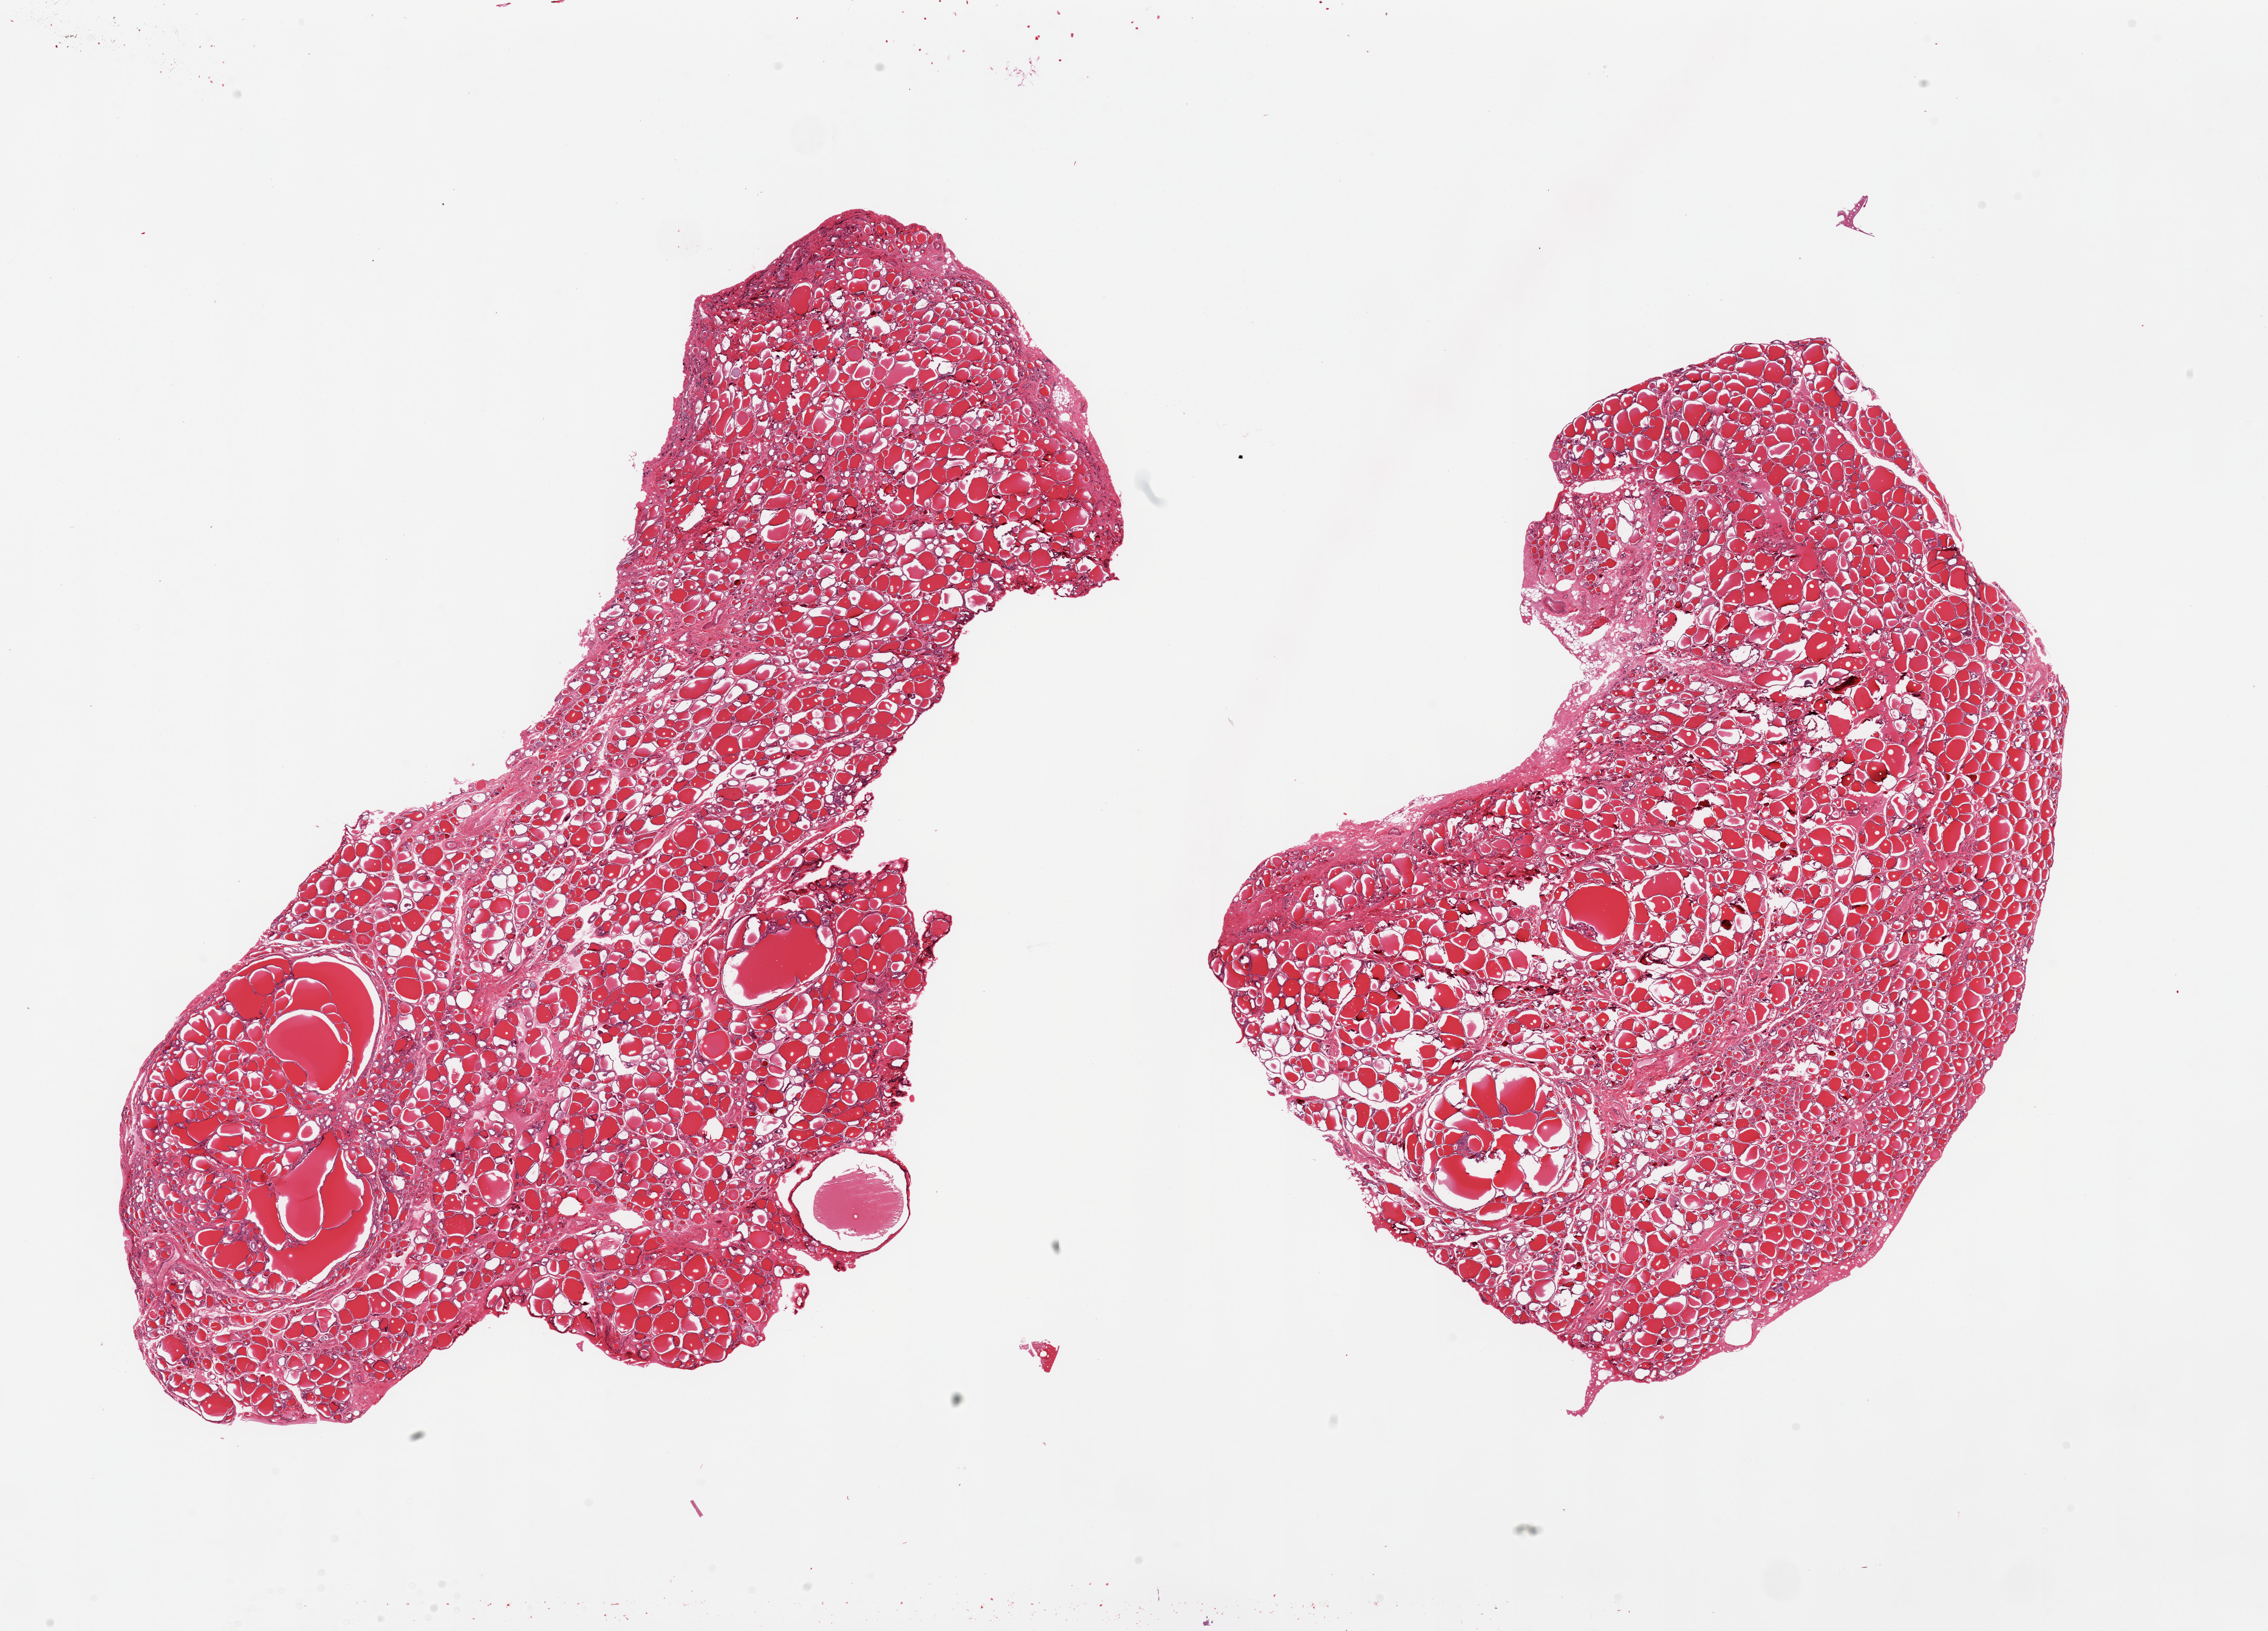
H&E whole-slide image, shown as a low-resolution overview of the whole scanned area (about 29.5 x 21.2 mm, acquisition: 20x scan). PAXgene-fixed paraffin-embedded (PFPE) section. Section of thyroid (target tissue). Donor tissue sample. Donor sex: female.
Reviewer comment on this tissue sample: 2 pieces, some nodular change.